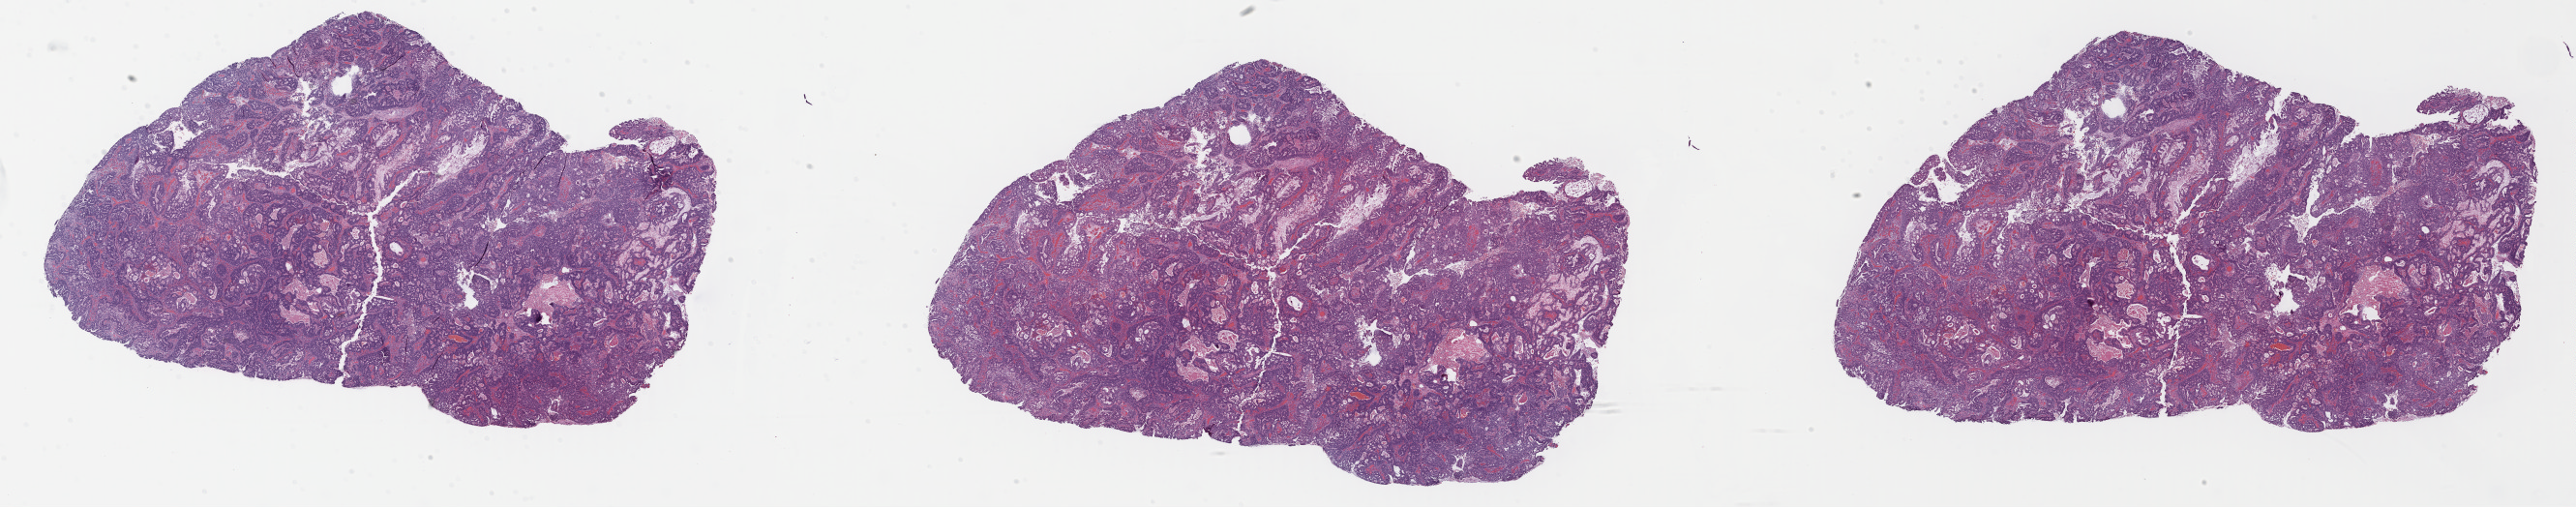
Hematoxylin and eosin (H&E) stained whole-slide image — shown as a low-resolution overview of the whole scanned area (about 41.9 x 8.2 mm, acquisition: 40x scan). Formalin-fixed paraffin-embedded (FFPE) diagnostic section. Primary tumour sample from the esophagus. Patient: male, age at initial diagnosis 62 years. Histologic grade: G2 (moderately differentiated).
* lymph nodes positive (case pathology): 15 of 20 examined
* AJCC pathologic stage: IIIC (7th edition)
* pathologic diagnosis: Adenocarcinoma, NOS